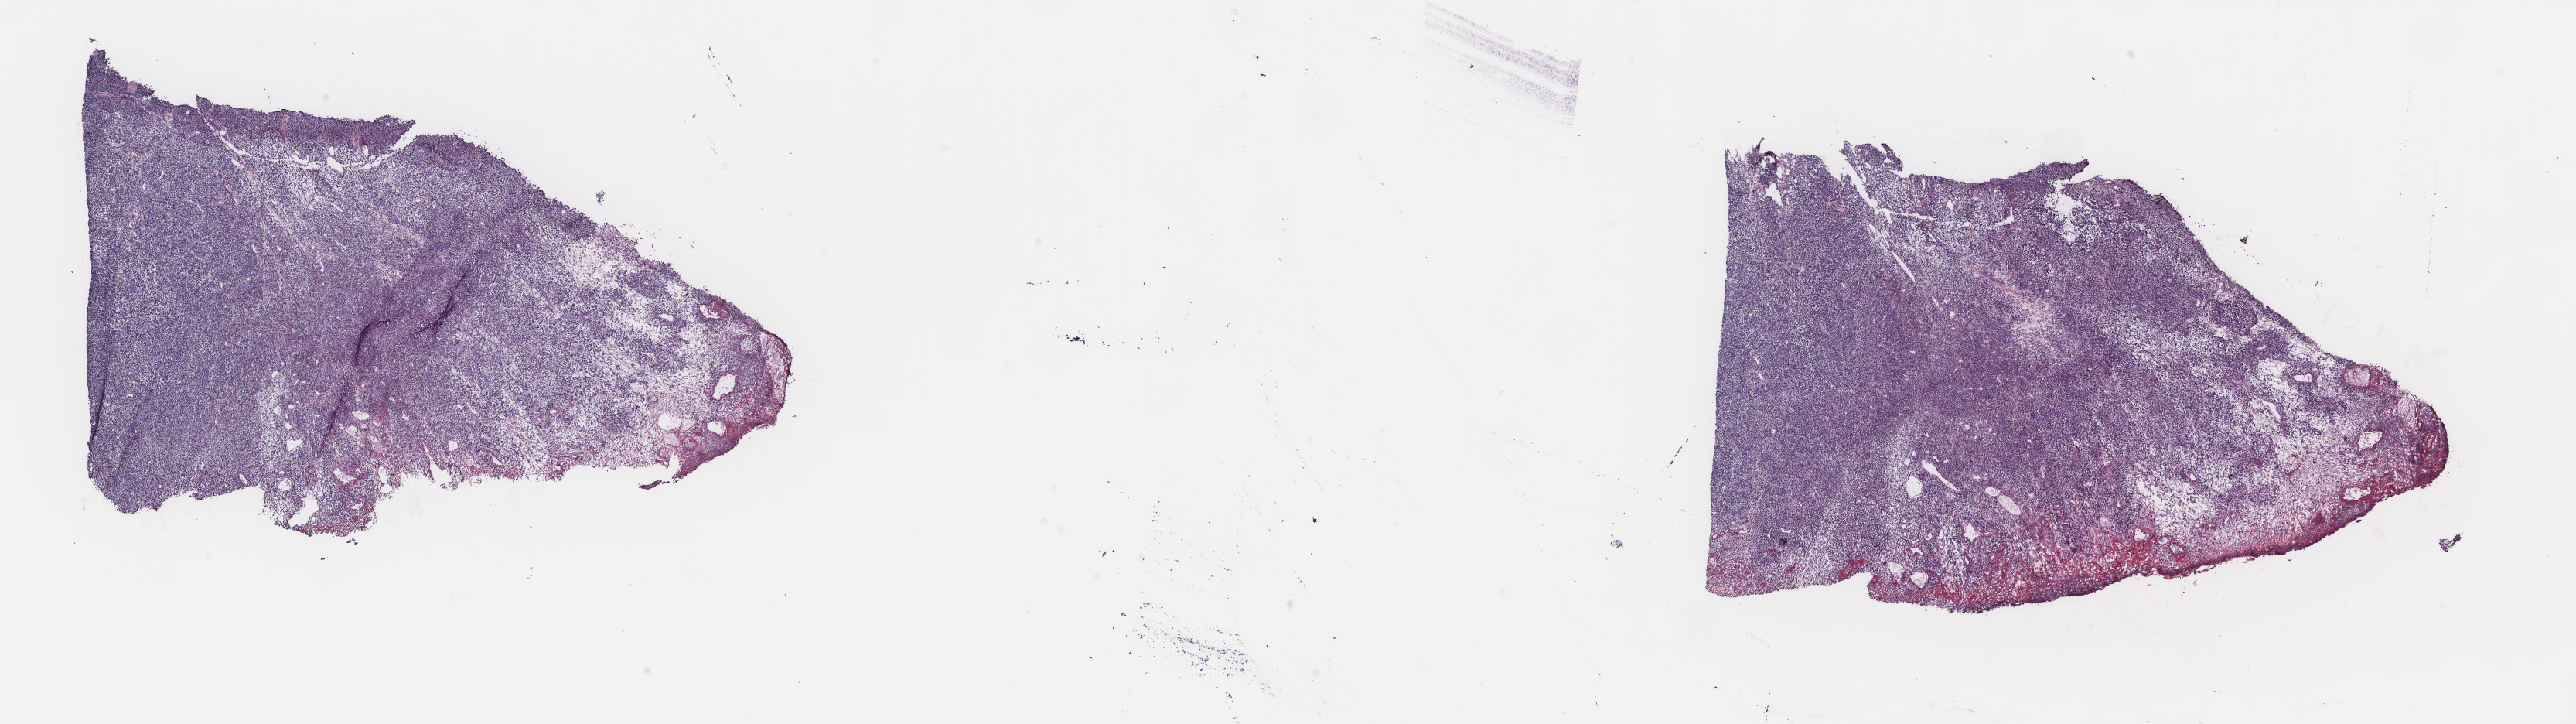
Digitized H&E tissue section (whole slide), whole scanned area (about 26.4 x 7.4 mm, from a 40x scan) shown as a low-resolution overview, frozen section, skin, primary tumour sample. Patient: female, age at initial diagnosis 73 years. Pathologist review of this section (percent, as recorded): tumour cells 95%, tumour nuclei 85%, normal cells 0%, stromal cells 0%, necrosis 5%. Inflammatory infiltration, as recorded: lymphocyte infiltration 3%, monocyte infiltration 0%, neutrophil infiltration 0%.
• TNM: T4b N0 M0
• AJCC pathologic stage: IIC (7th edition)
• pathologic diagnosis: Malignant melanoma, NOS